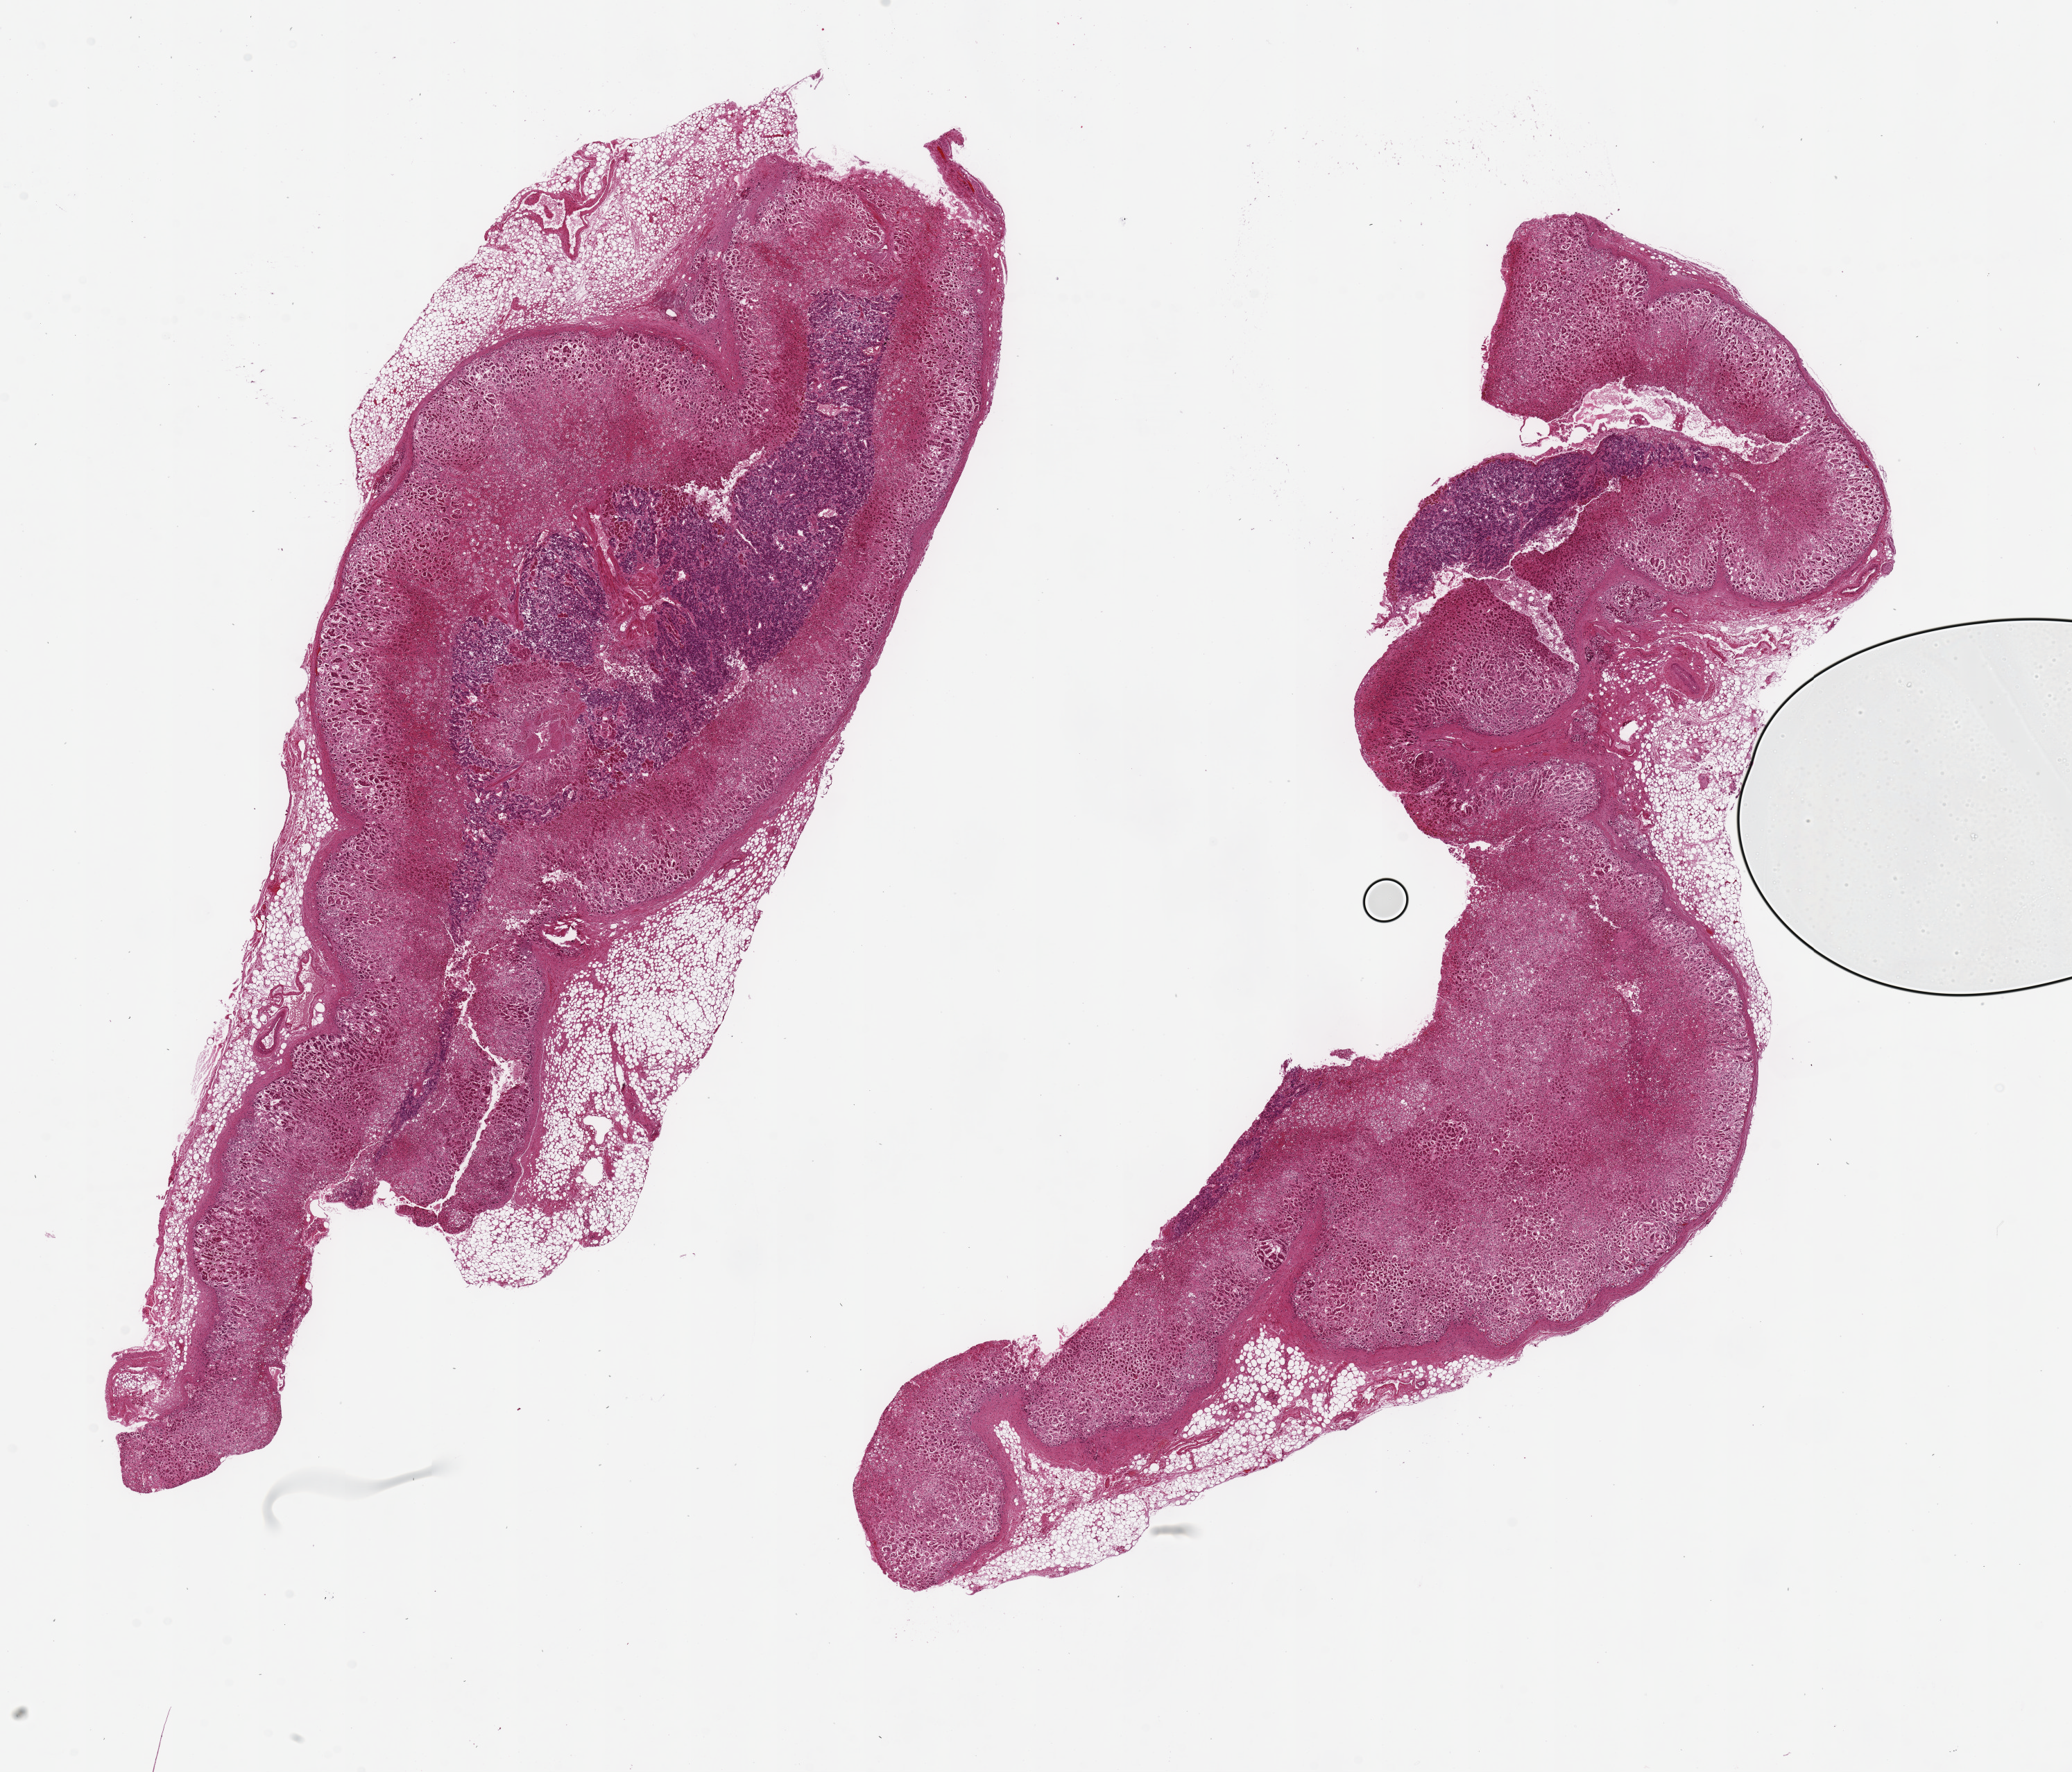
Hematoxylin and eosin (H&E) whole-slide image — shown as a low-resolution overview of the whole scanned area (about 23.6 x 20.2 mm). PAXgene-fixed, paraffin-embedded tissue. Section of adrenal gland (target tissue). Donor tissue sample. Male donor.
Review note (as recorded): 2 pieces, 18x7 & 17x5.5mm.